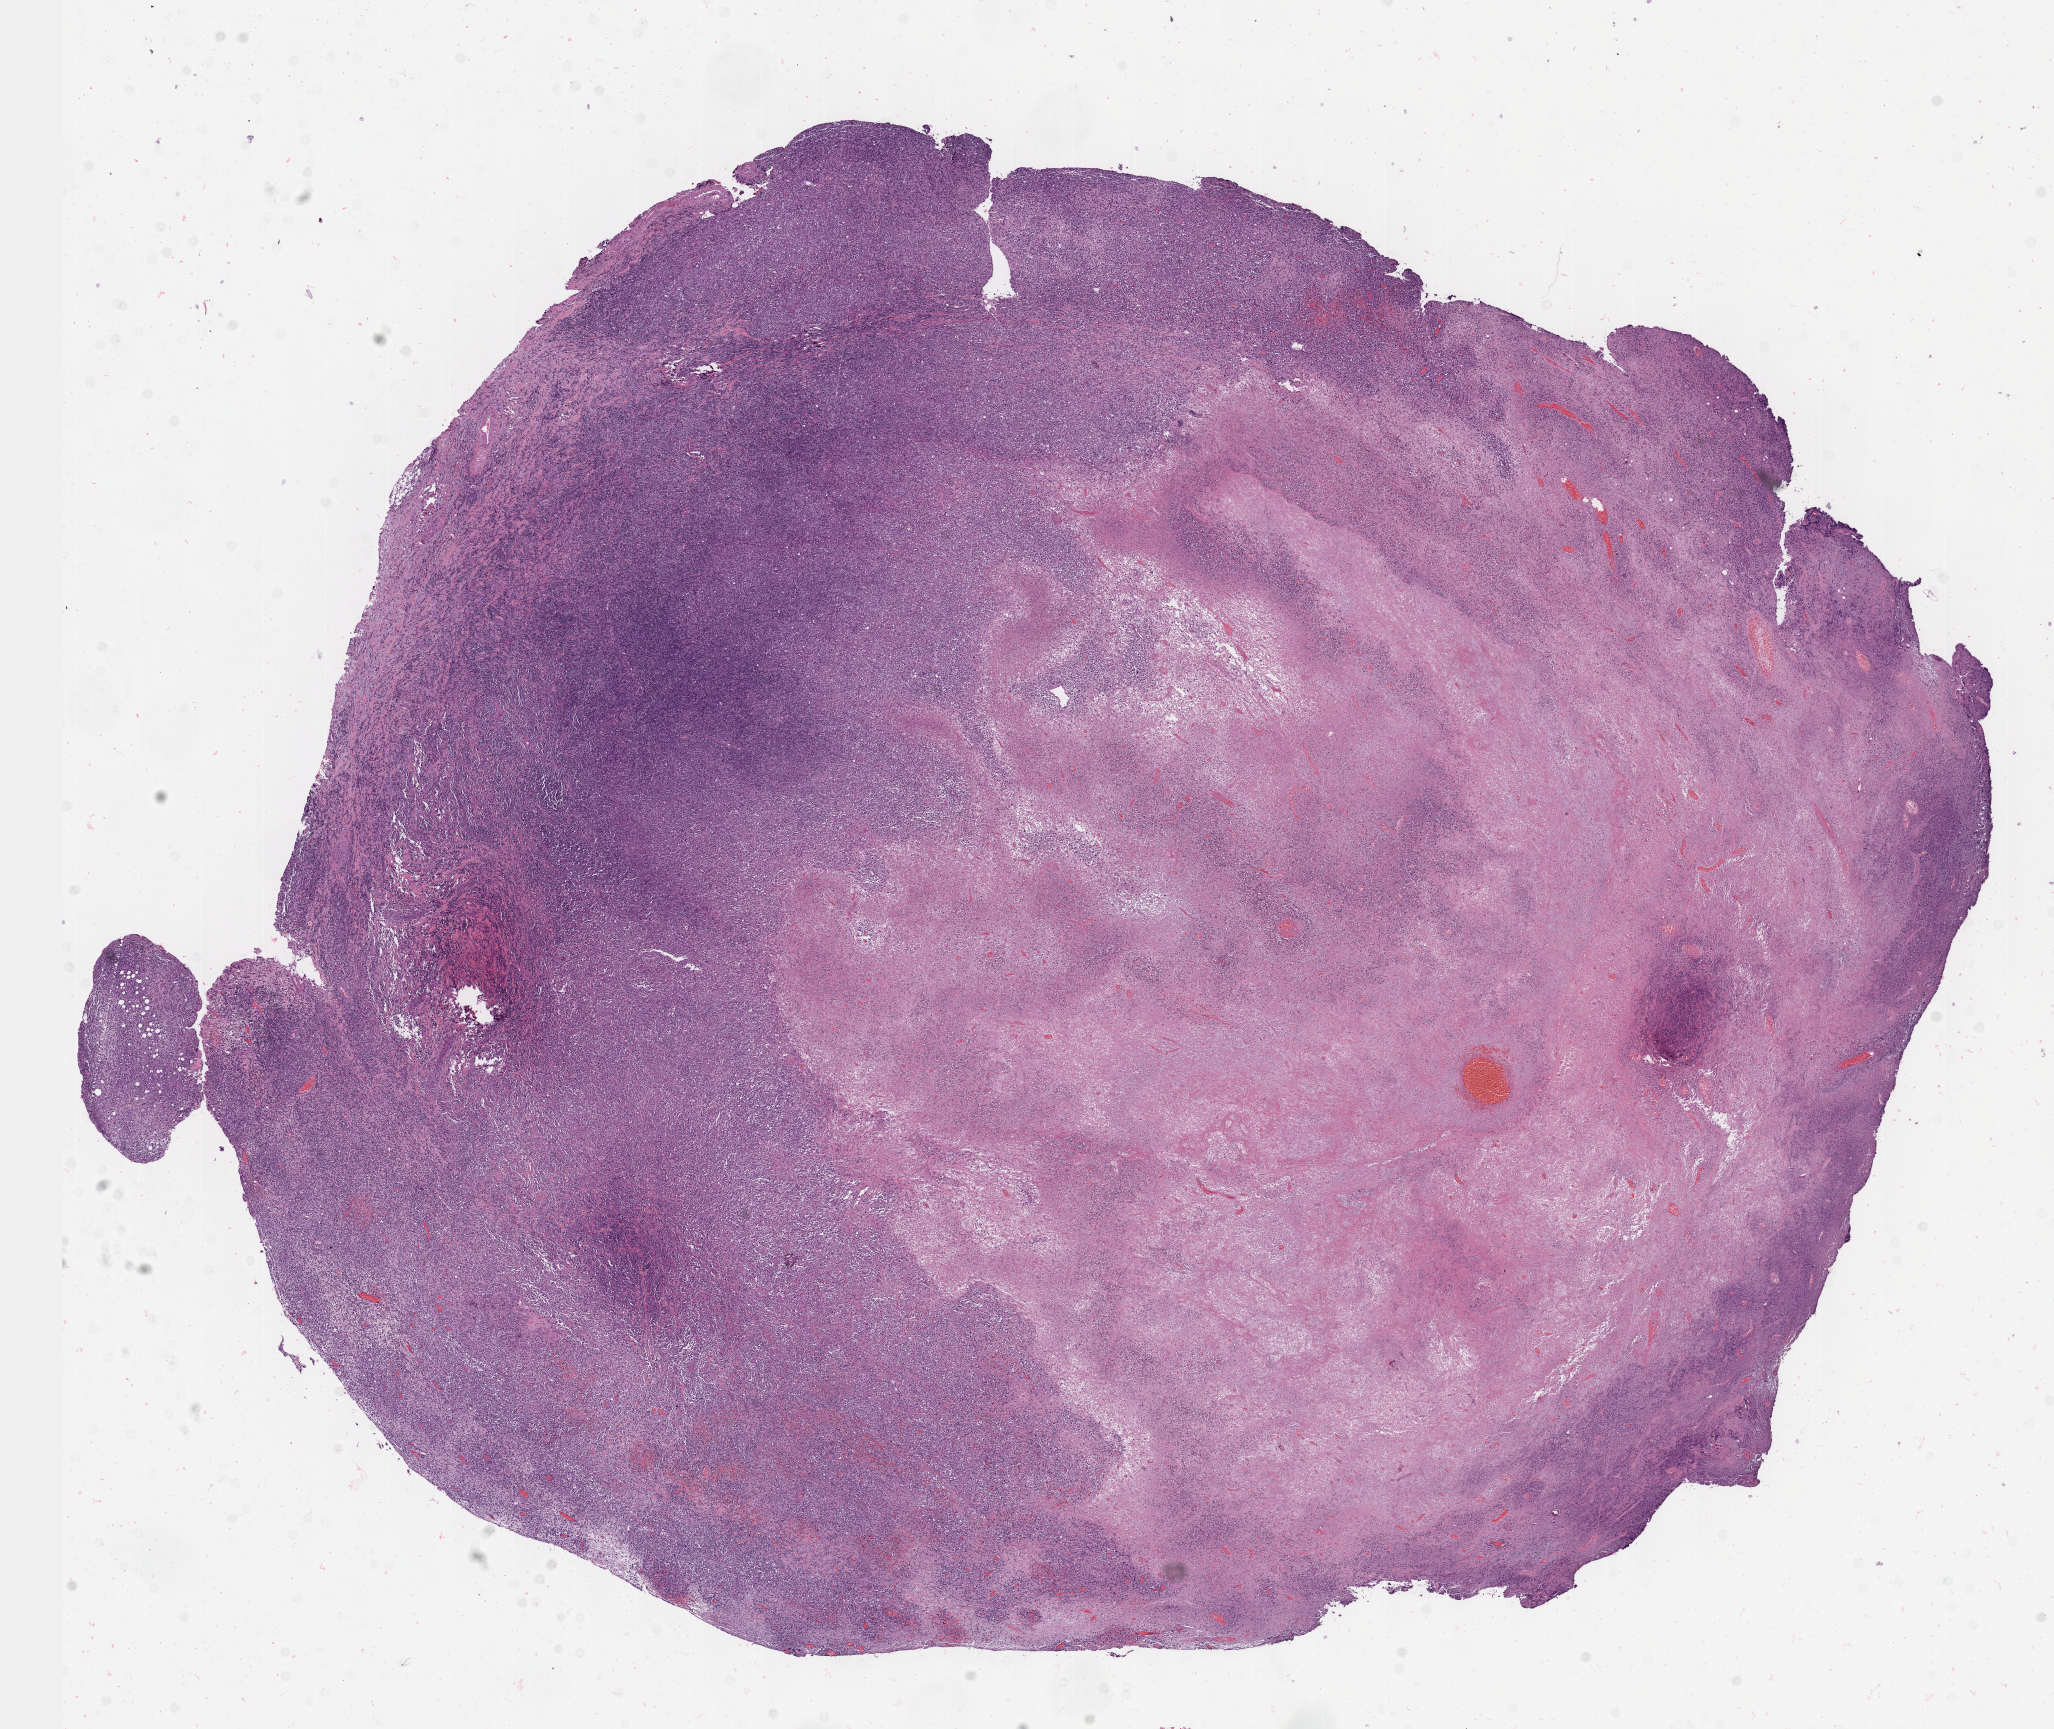
Whole-slide histology image, Hematoxylin and eosin (H&E) stained — shown as a low-resolution overview of the whole scanned area (about 16.6 x 14.0 mm, from a 40x scan), formalin-fixed paraffin-embedded (FFPE) diagnostic section, sample: primary tumour, lymphoid tissue. Female, age 27 years at initial diagnosis.
• pathologic diagnosis: Diffuse large B-cell lymphoma, NOS